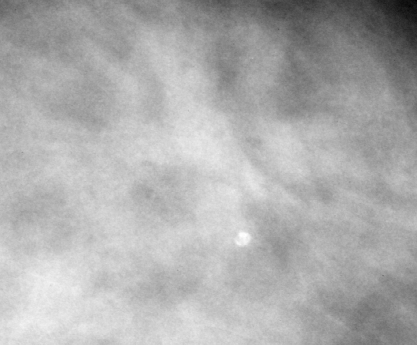
Region of interest cut from a scanned film mammogram (one marked finding); left breast; CC view.
- Marked abnormality: mass, shape architectural distortion, margins ill defined; BI-RADS assessment category 4; pathology (as recorded): malignant.